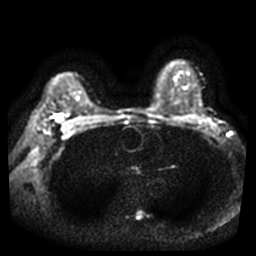
Breast MRI, one axial slice; slice 30 of 44 in the series (ordered by position); diffusion-weighted series; image 2 of 4 stored at this slice position (different b-values; order by instance number); 3 T; 5 mm slice thickness; 256 × 256 image matrix. Female patient.
Structures marked on this image (manually delineated by an expert):
- tumour on diffusion-weighted imaging: bounding box <57,115,61,121> (left, top, right, bottom; pixels)